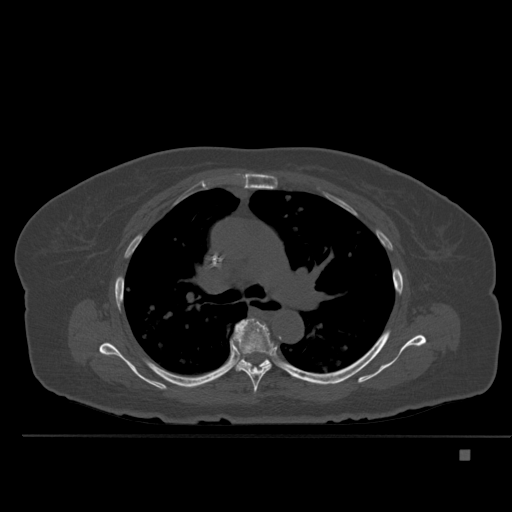
CT including the spine, one axial slice. Position 349 of 477 along the scan axis. Bone window (W 1800 / L 400 HU). 1.5 mm slice thickness. 512 × 512 image matrix, field of view 422 × 422 mm. Female patient, age 74 years. From the clinical record (not read from this slice): primary cancer: colon.
Structures marked on this image (semi-automatic segmentation, software-assisted and operator-edited):
- T5 vertebra: bounding box [x1, y1, x2, y2] px = [233, 318, 275, 394]
- T6 vertebra: [231, 323, 271, 369]